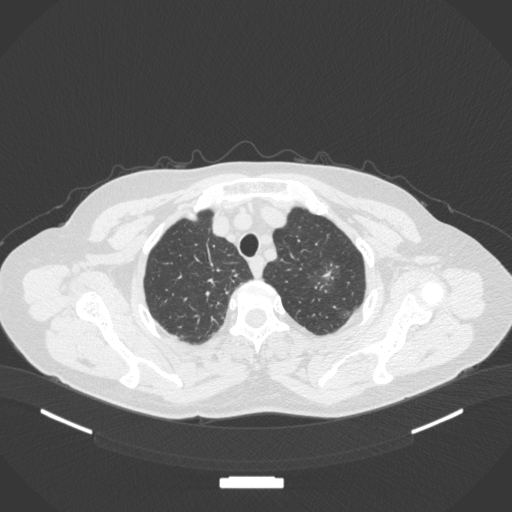
Chest CT, one axial slice. Slice 308 of 369 in the series (ordered by position). Lung window (W 1500 / L -600 HU). 512 × 512 image matrix, field of view 400 × 400 mm. Female patient, age 64 years. From the clinical record (not read from this slice): clinical TNM (as recorded): T1c N0 M0.
Structures marked on this image (bounding box drawn by a radiologist):
- lung tumour (recorded histology: adenocarcinoma): bounding box <306,254,345,300> (left, top, right, bottom; pixels)